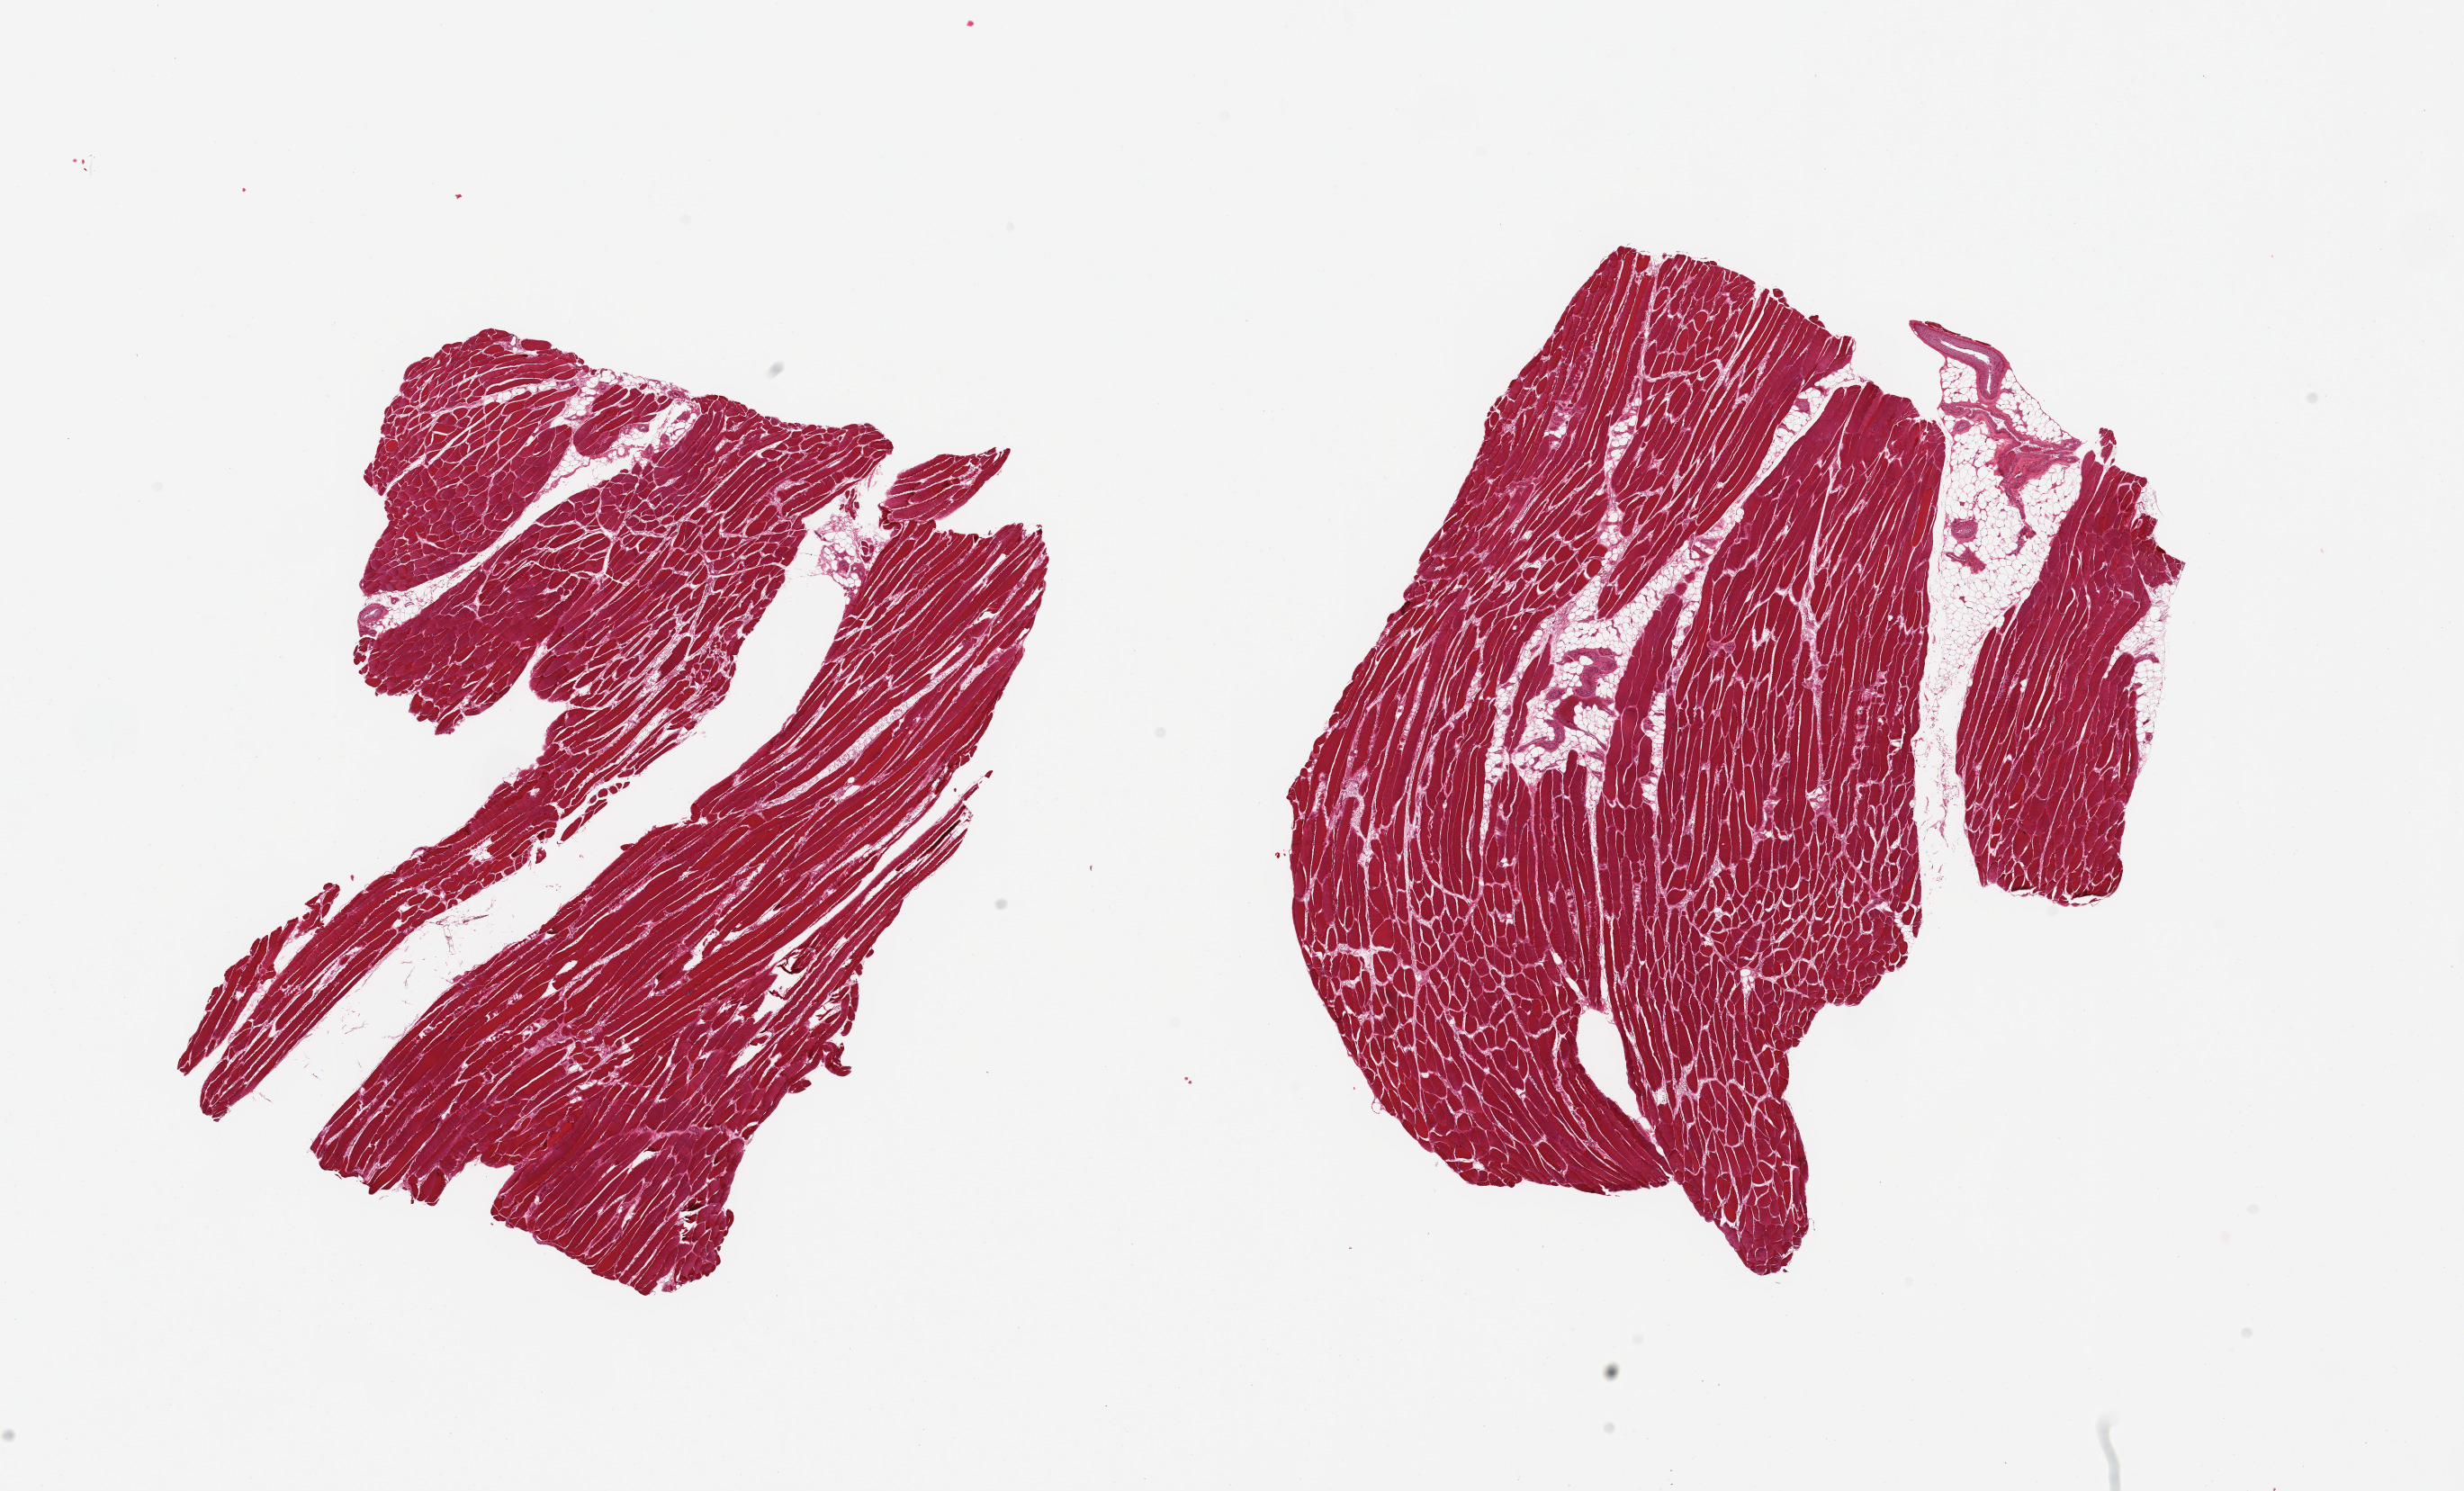
Digitized hematoxylin and eosin (H&E)-stained section, brightfield, shown as a low-resolution overview of the whole scanned area (about 21.7 x 13.1 mm, from a 20x scan), PAXgene-fixed paraffin-embedded (PFPE) section, section of skeletal muscle (target tissue), tissue donor sample. Donor sex: female.
* pathologist's review note for this sample: 2 pieces, interstitial fat/vascular elements is ~10% total tissue